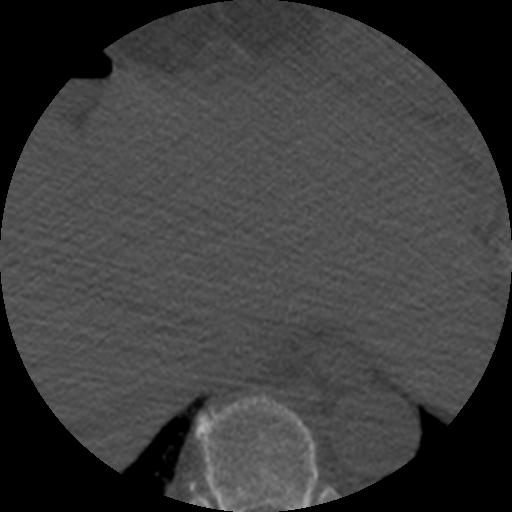
CT including the spine, one axial slice. Position 294 of 508 along the scan axis. Reconstruction kernel STANDARD. 120 kVp. Bone window (W 1800 / L 400 HU). 512 × 512 image matrix, field of view 160 × 160 mm. Patient age 57 years. Case-level facts recorded for this patient, not image findings: primary cancer: prostate.
Outlined on this slice (semi-automatically segmented with operator editing):
- T9 vertebra: box from (x=195, y=395) to (x=317, y=512) px